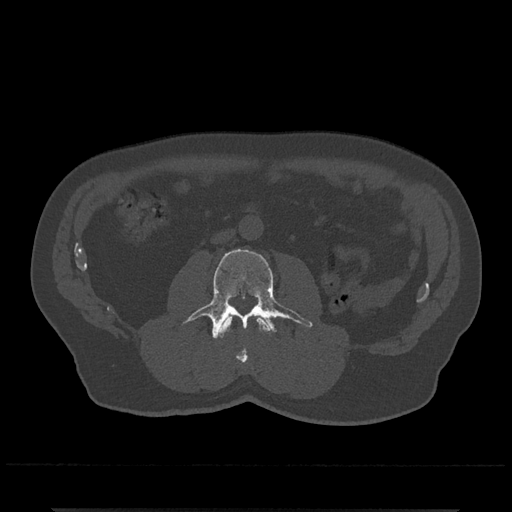
CT including the spine, one axial slice; position 234 of 797 along the scan axis; reconstruction kernel Br40s/3; 120 kVp; bone window (W 1800 / L 400 HU); 0.5 mm slice thickness; 512 × 512 image matrix, field of view 393 × 393 mm. Male patient, age 67 years. From the clinical record (not read from this slice): primary cancer: prostate.
Annotated regions visible in this slice (semi-automatically segmented with operator editing):
- L2 vertebra: bounding box [x1, y1, x2, y2] px = [218, 315, 270, 363]
- L3 vertebra: [186, 249, 313, 339]